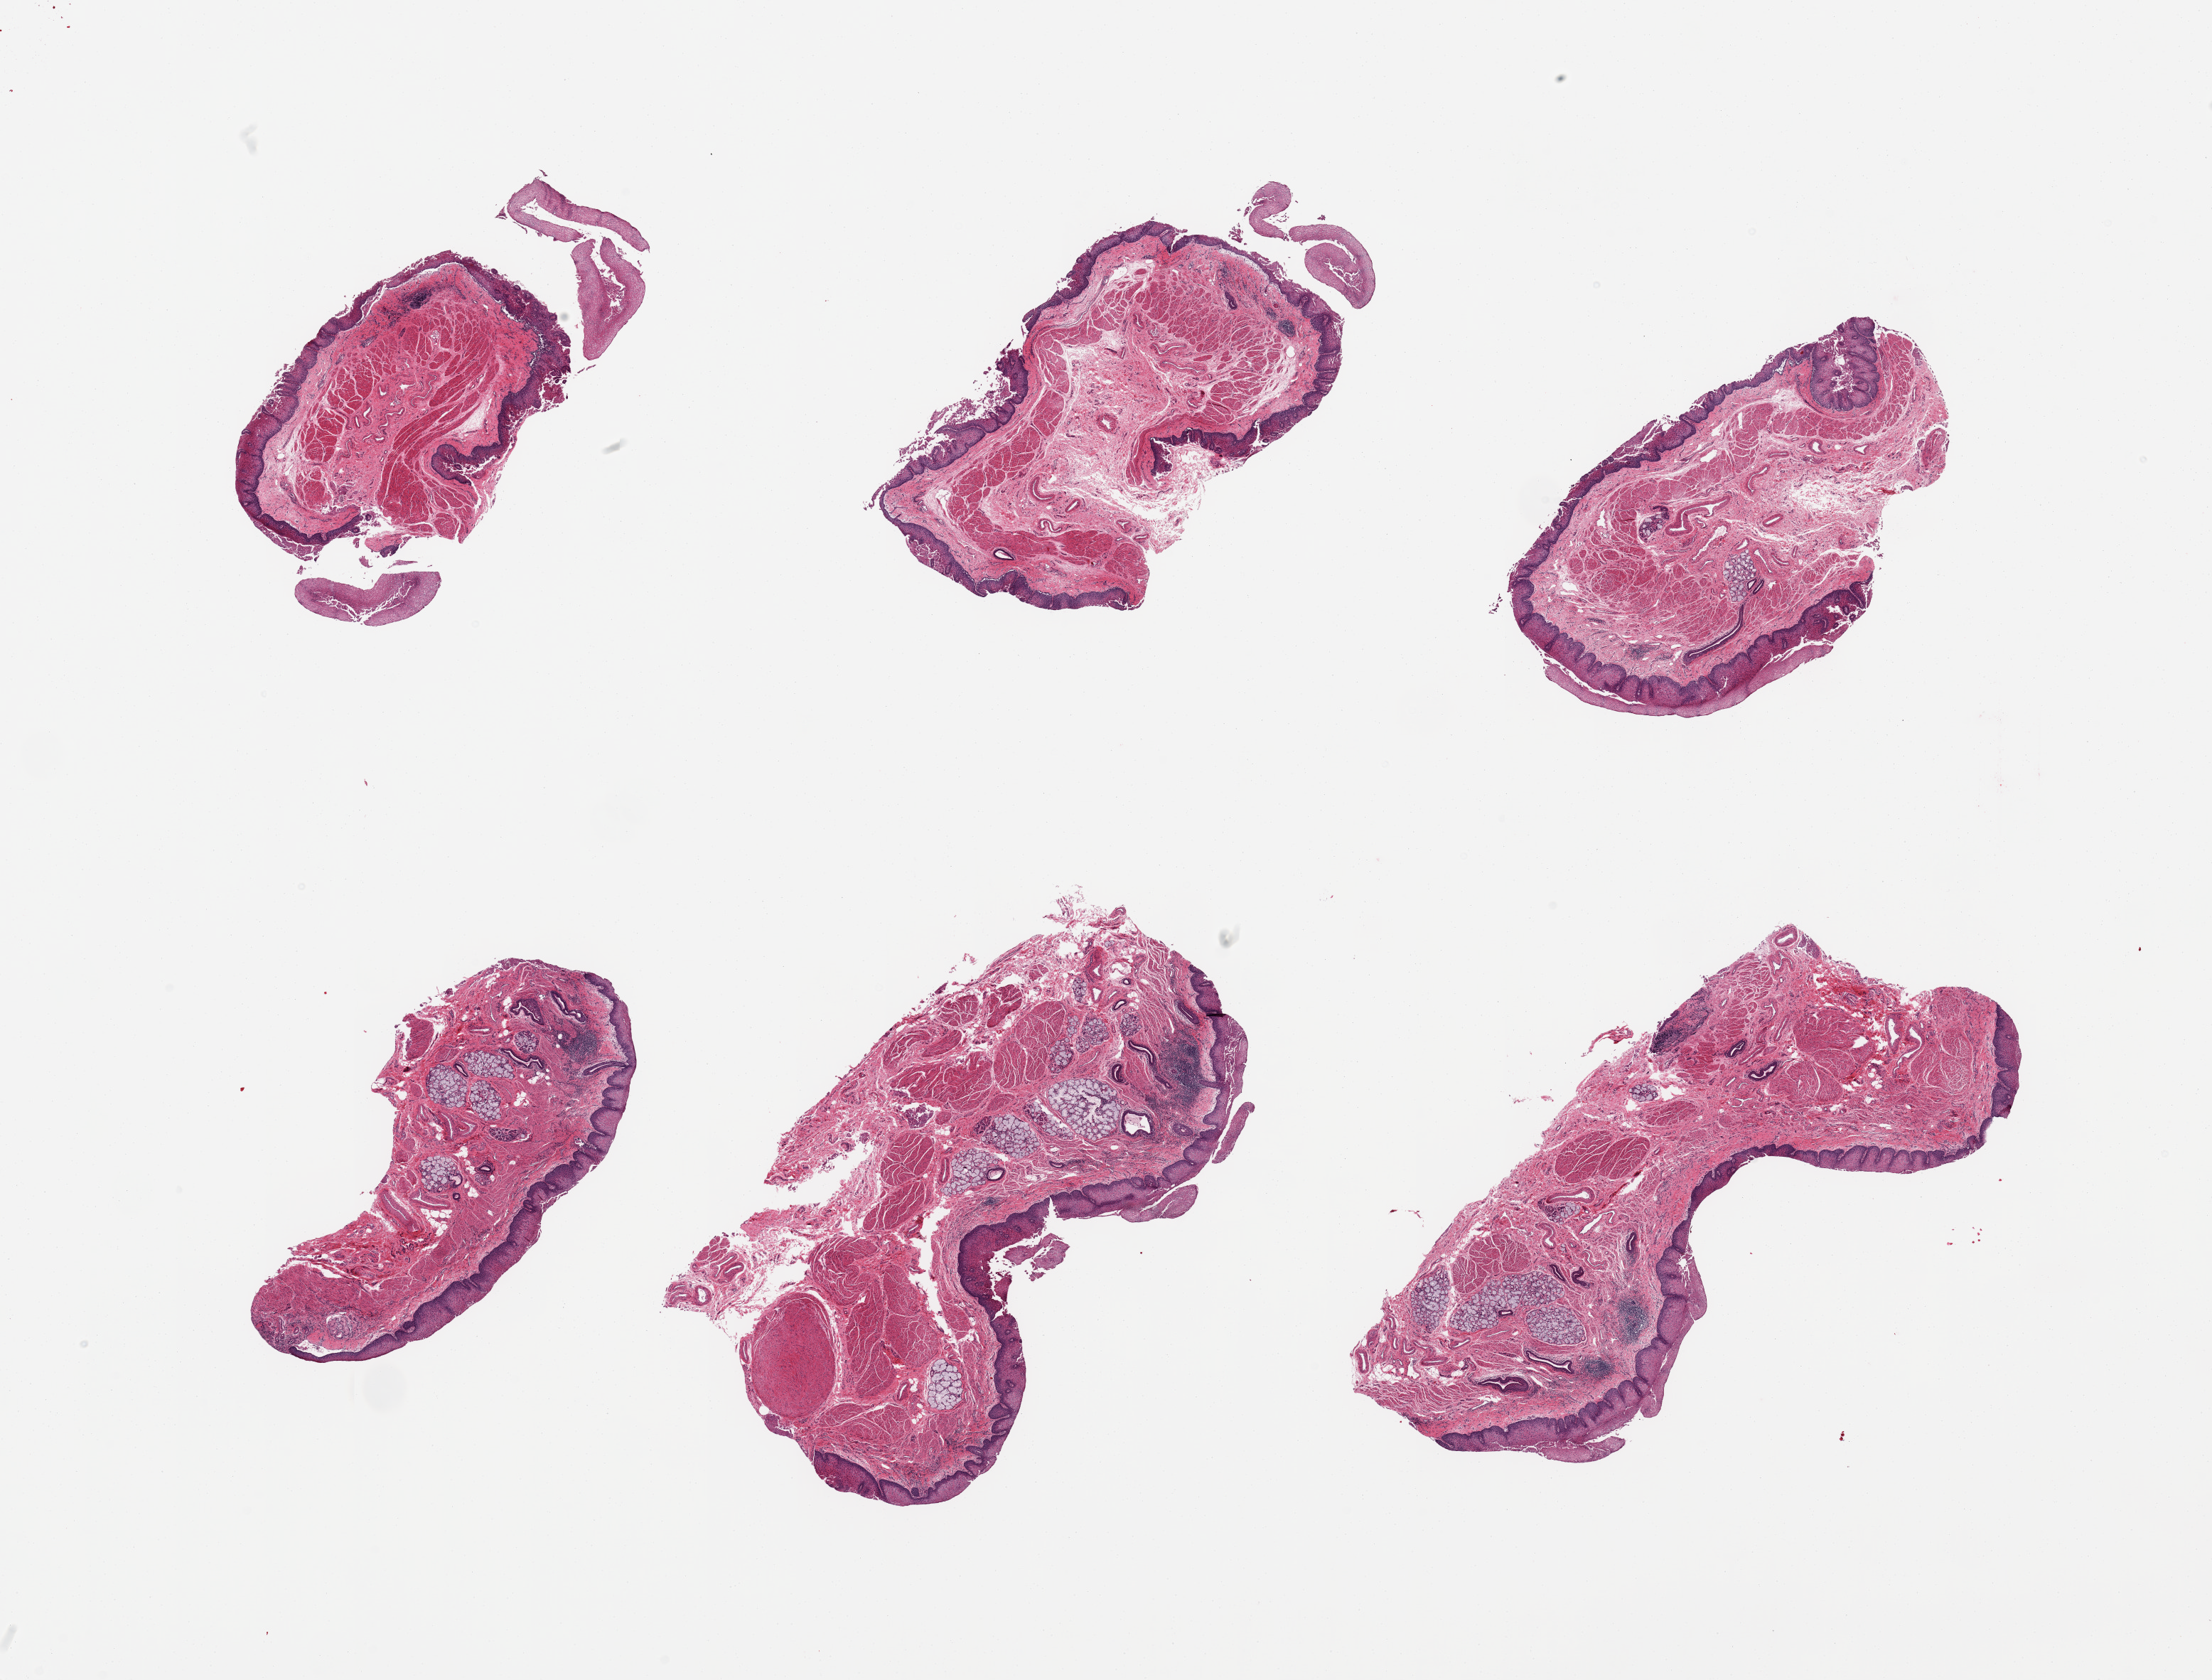
Digitized haematoxylin and eosin-stained section, shown as a low-resolution overview of the whole scanned area (about 24.6 x 18.7 mm, from a 20x scan). PAXgene-fixed paraffin-embedded (PFPE) section. Section of esophageal mucous membrane (target tissue). Donor tissue sample.
• pathologist's review note for this sample: 6 pieces; surface epithelium desquamation and focal epithelial dissociation; squamous mucosa ~ 0.3mm thick; submucosal mucus glands and focal lymphocytic aggregates in submucosa; taken at GE junction (not target region 4 cm above), small leiomyoma